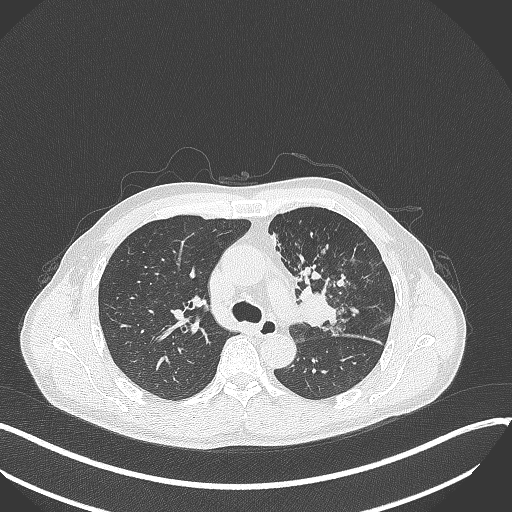
Chest CT, one axial slice; position 226 of 411 along the scan axis; reconstruction kernel B70f; 120 kVp; lung window (W 1500 / L -600 HU); 512 × 512 image matrix, field of view 400 × 400 mm. Male patient, age 56 years. Case-level facts recorded for this patient, not image findings: clinical TNM (as recorded): T2a N0 M0.
Structures marked on this image (bounding box drawn by a radiologist):
- lung tumour (recorded histology: squamous cell carcinoma): bounding box (x1, y1, x2, y2) in pixels: (297, 282, 350, 341)